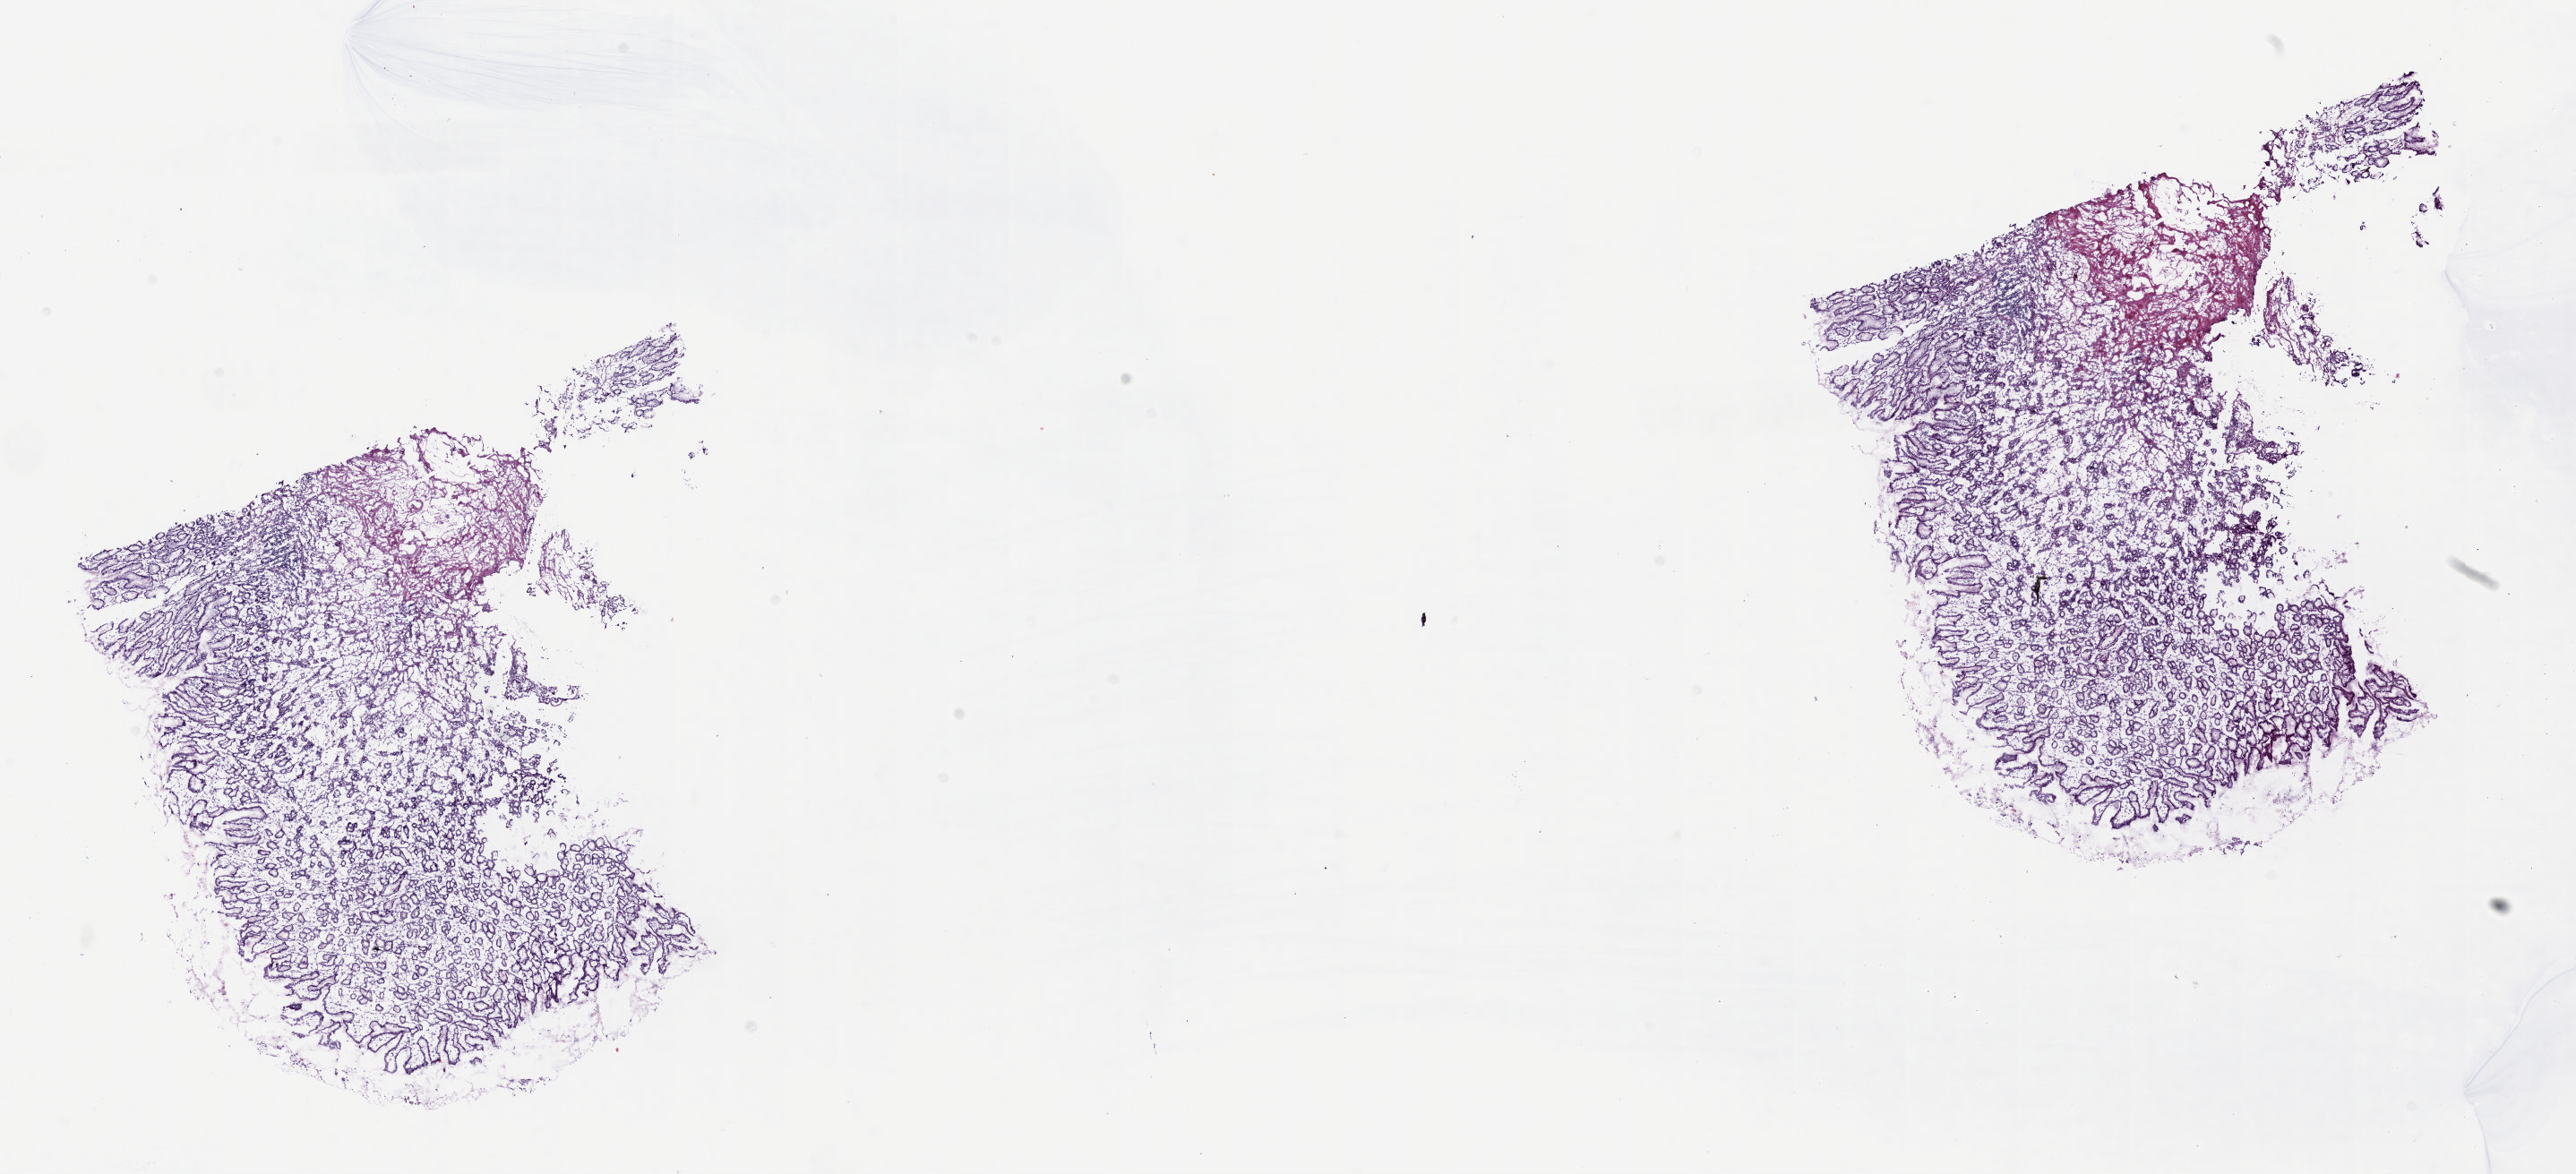
Whole-slide histology image, H&E-stained — shown as a low-resolution overview of the whole scanned area (about 22.8 x 10.4 mm, from a 20x scan), frozen section from the top of the tissue portion, pancreas, solid tissue normal (non-tumour tissue) sample. Male patient; age at initial diagnosis 71 years. Pathologist review of this section (percent, as recorded): tumour cells 0%, tumour nuclei 0%, normal cells 40%, stromal cells 60%, necrosis 0%. Inflammatory infiltration, as recorded: lymphocyte infiltration 70%, monocyte infiltration 10%, neutrophil infiltration 10%.
- this section: solid tissue normal (non-tumour) sample from the same patient
- patient diagnosis: Infiltrating duct carcinoma, NOS (head of pancreas)